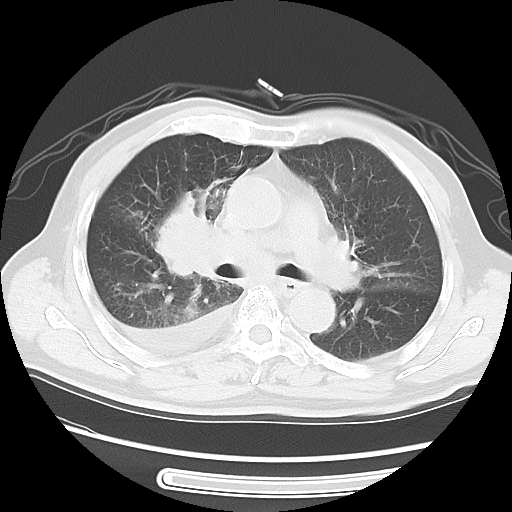
Chest CT, one axial slice. Reconstruction kernel LUNG. 120 kVp. Lung window (W 1500 / L -600 HU). 5 mm slice thickness. 512 × 512 image matrix. Patient: male, 77 years. Case-level facts recorded for this patient, not image findings: clinical TNM (as recorded): T3 N3 M1b.
Structures marked on this image (bounding box drawn by a radiologist):
- lung tumour (recorded histology: small cell carcinoma): bounding box <154,181,228,290> (left, top, right, bottom; pixels)